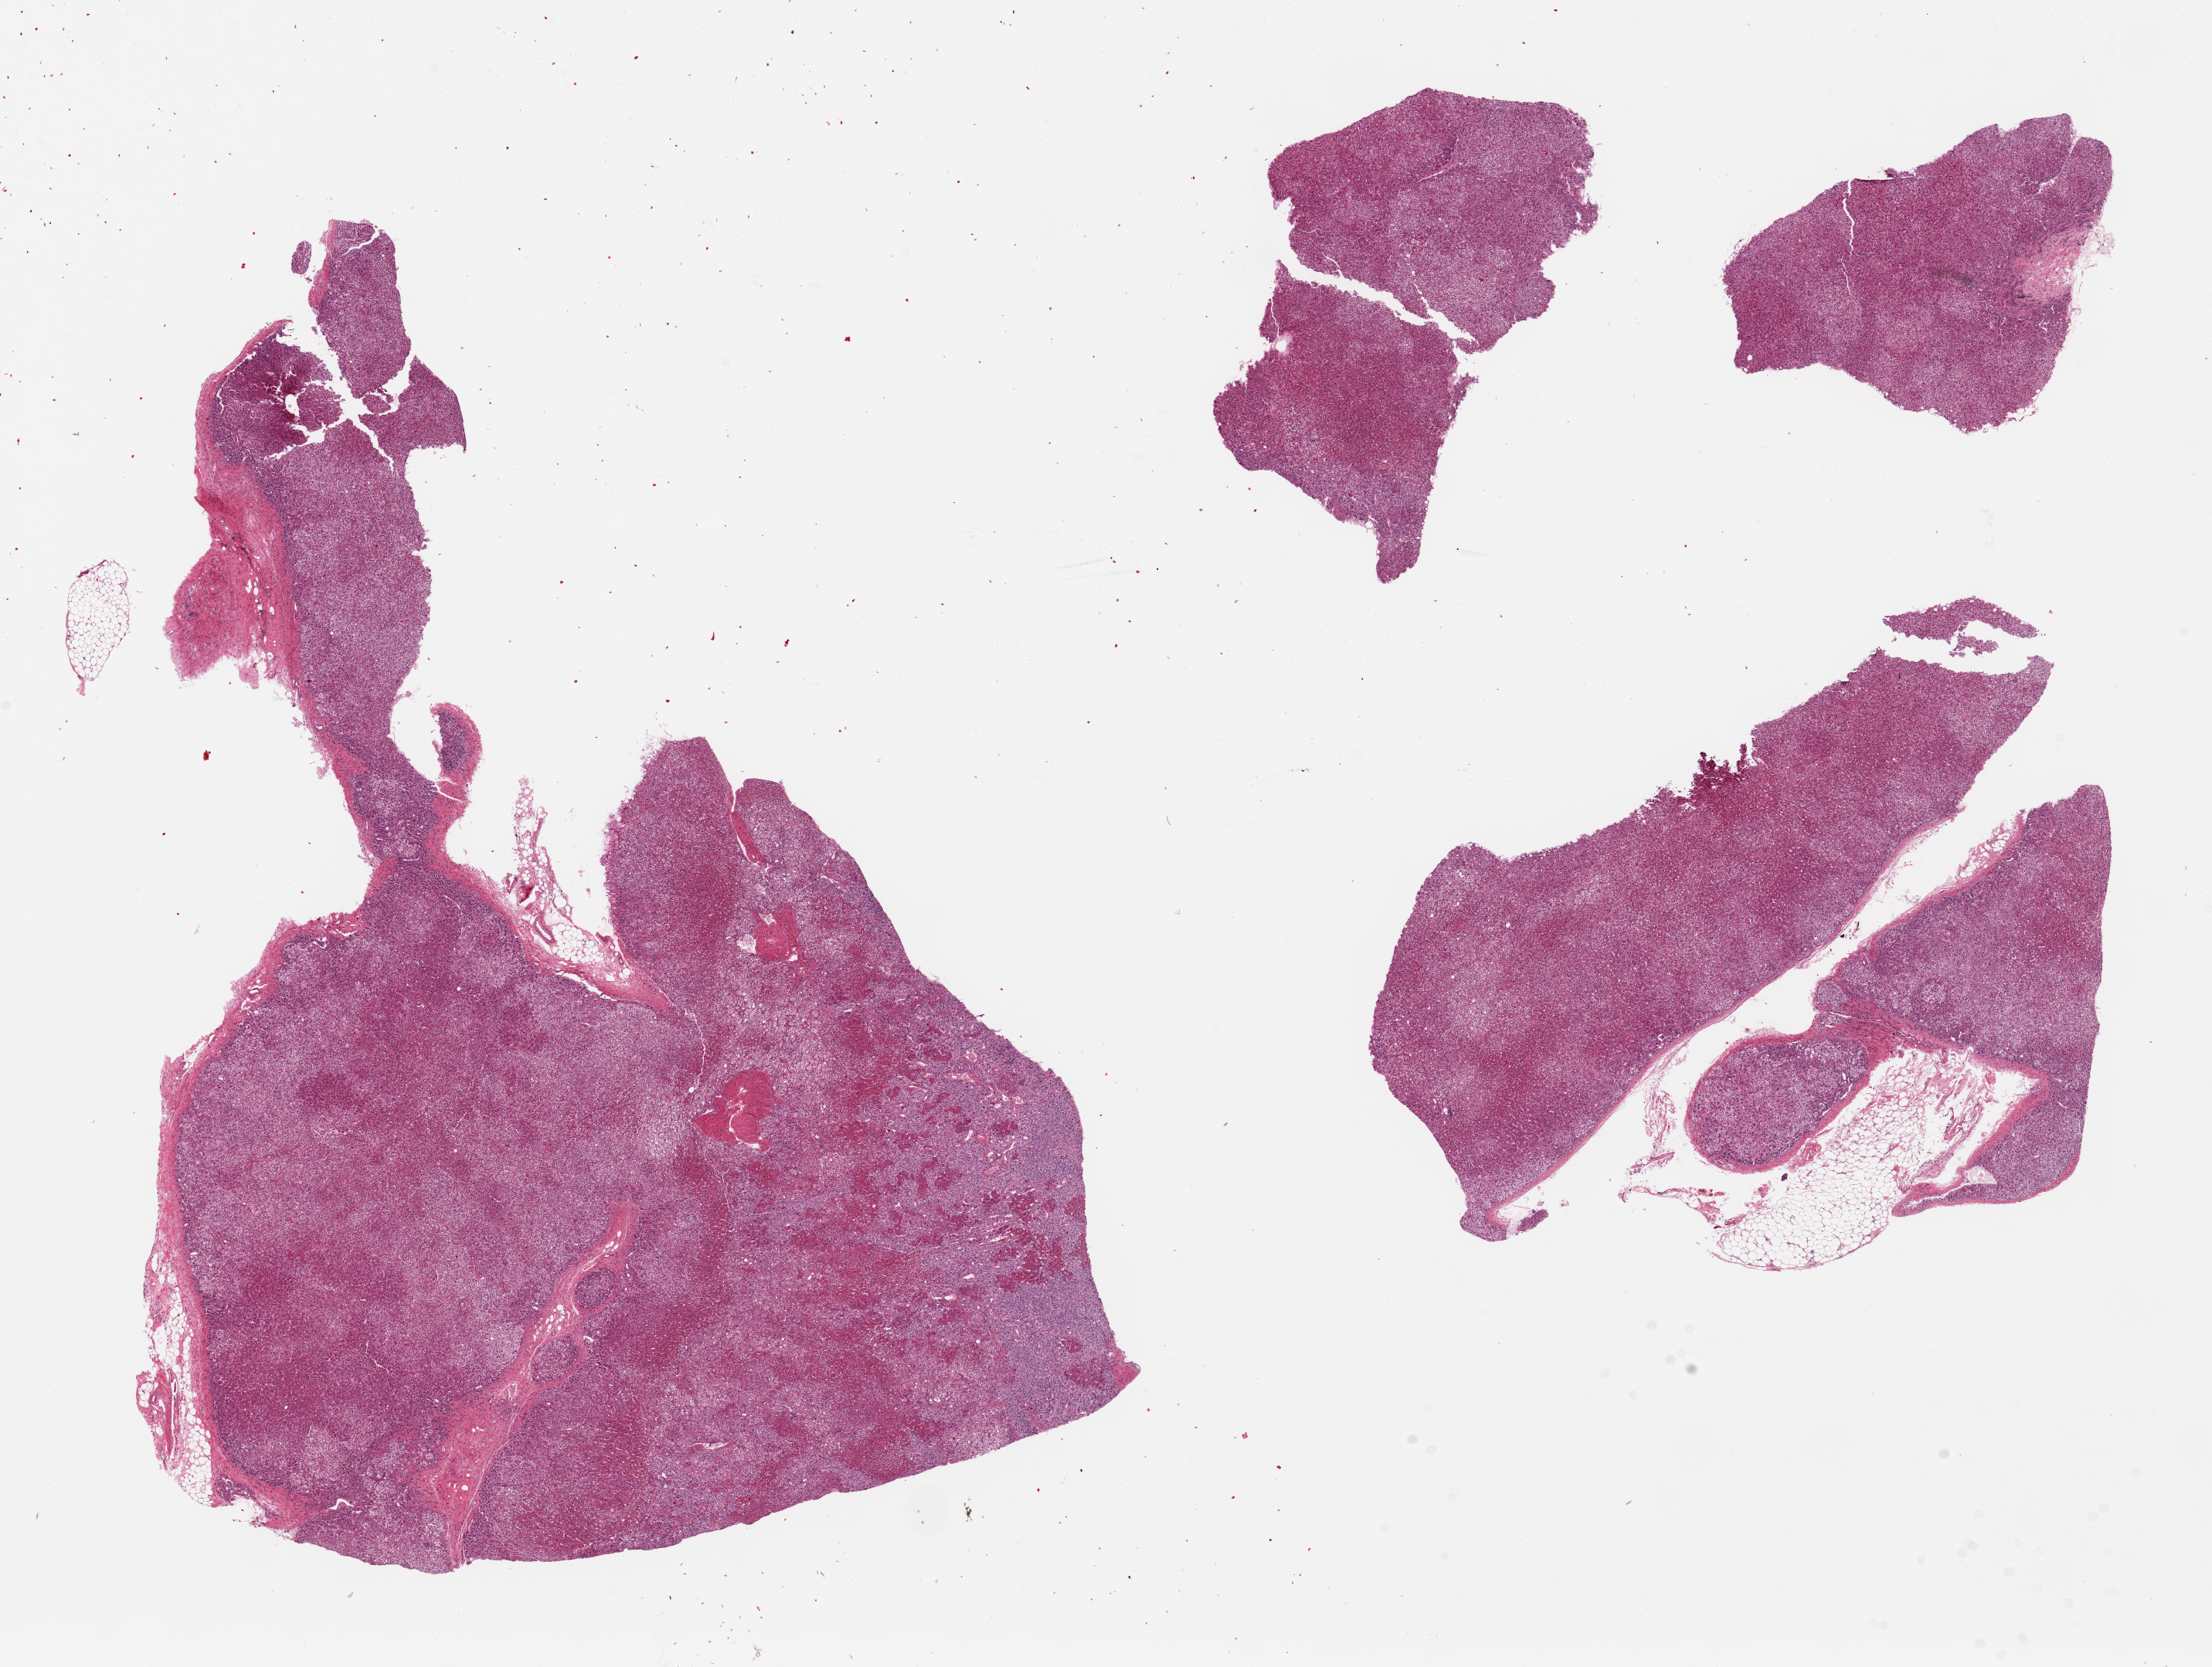
Hematoxylin and eosin (H&E) whole-slide image, shown as a low-resolution overview of the whole scanned area (about 22.6 x 17.1 mm); PAXgene-fixed paraffin-embedded (PFPE) section; target tissue: adrenal gland; tissue donor sample. Donor sex: male.
Review note (as recorded): 2 pieces, 14x10 & 12x9mm; all cortex, less than 10% adherent fat.